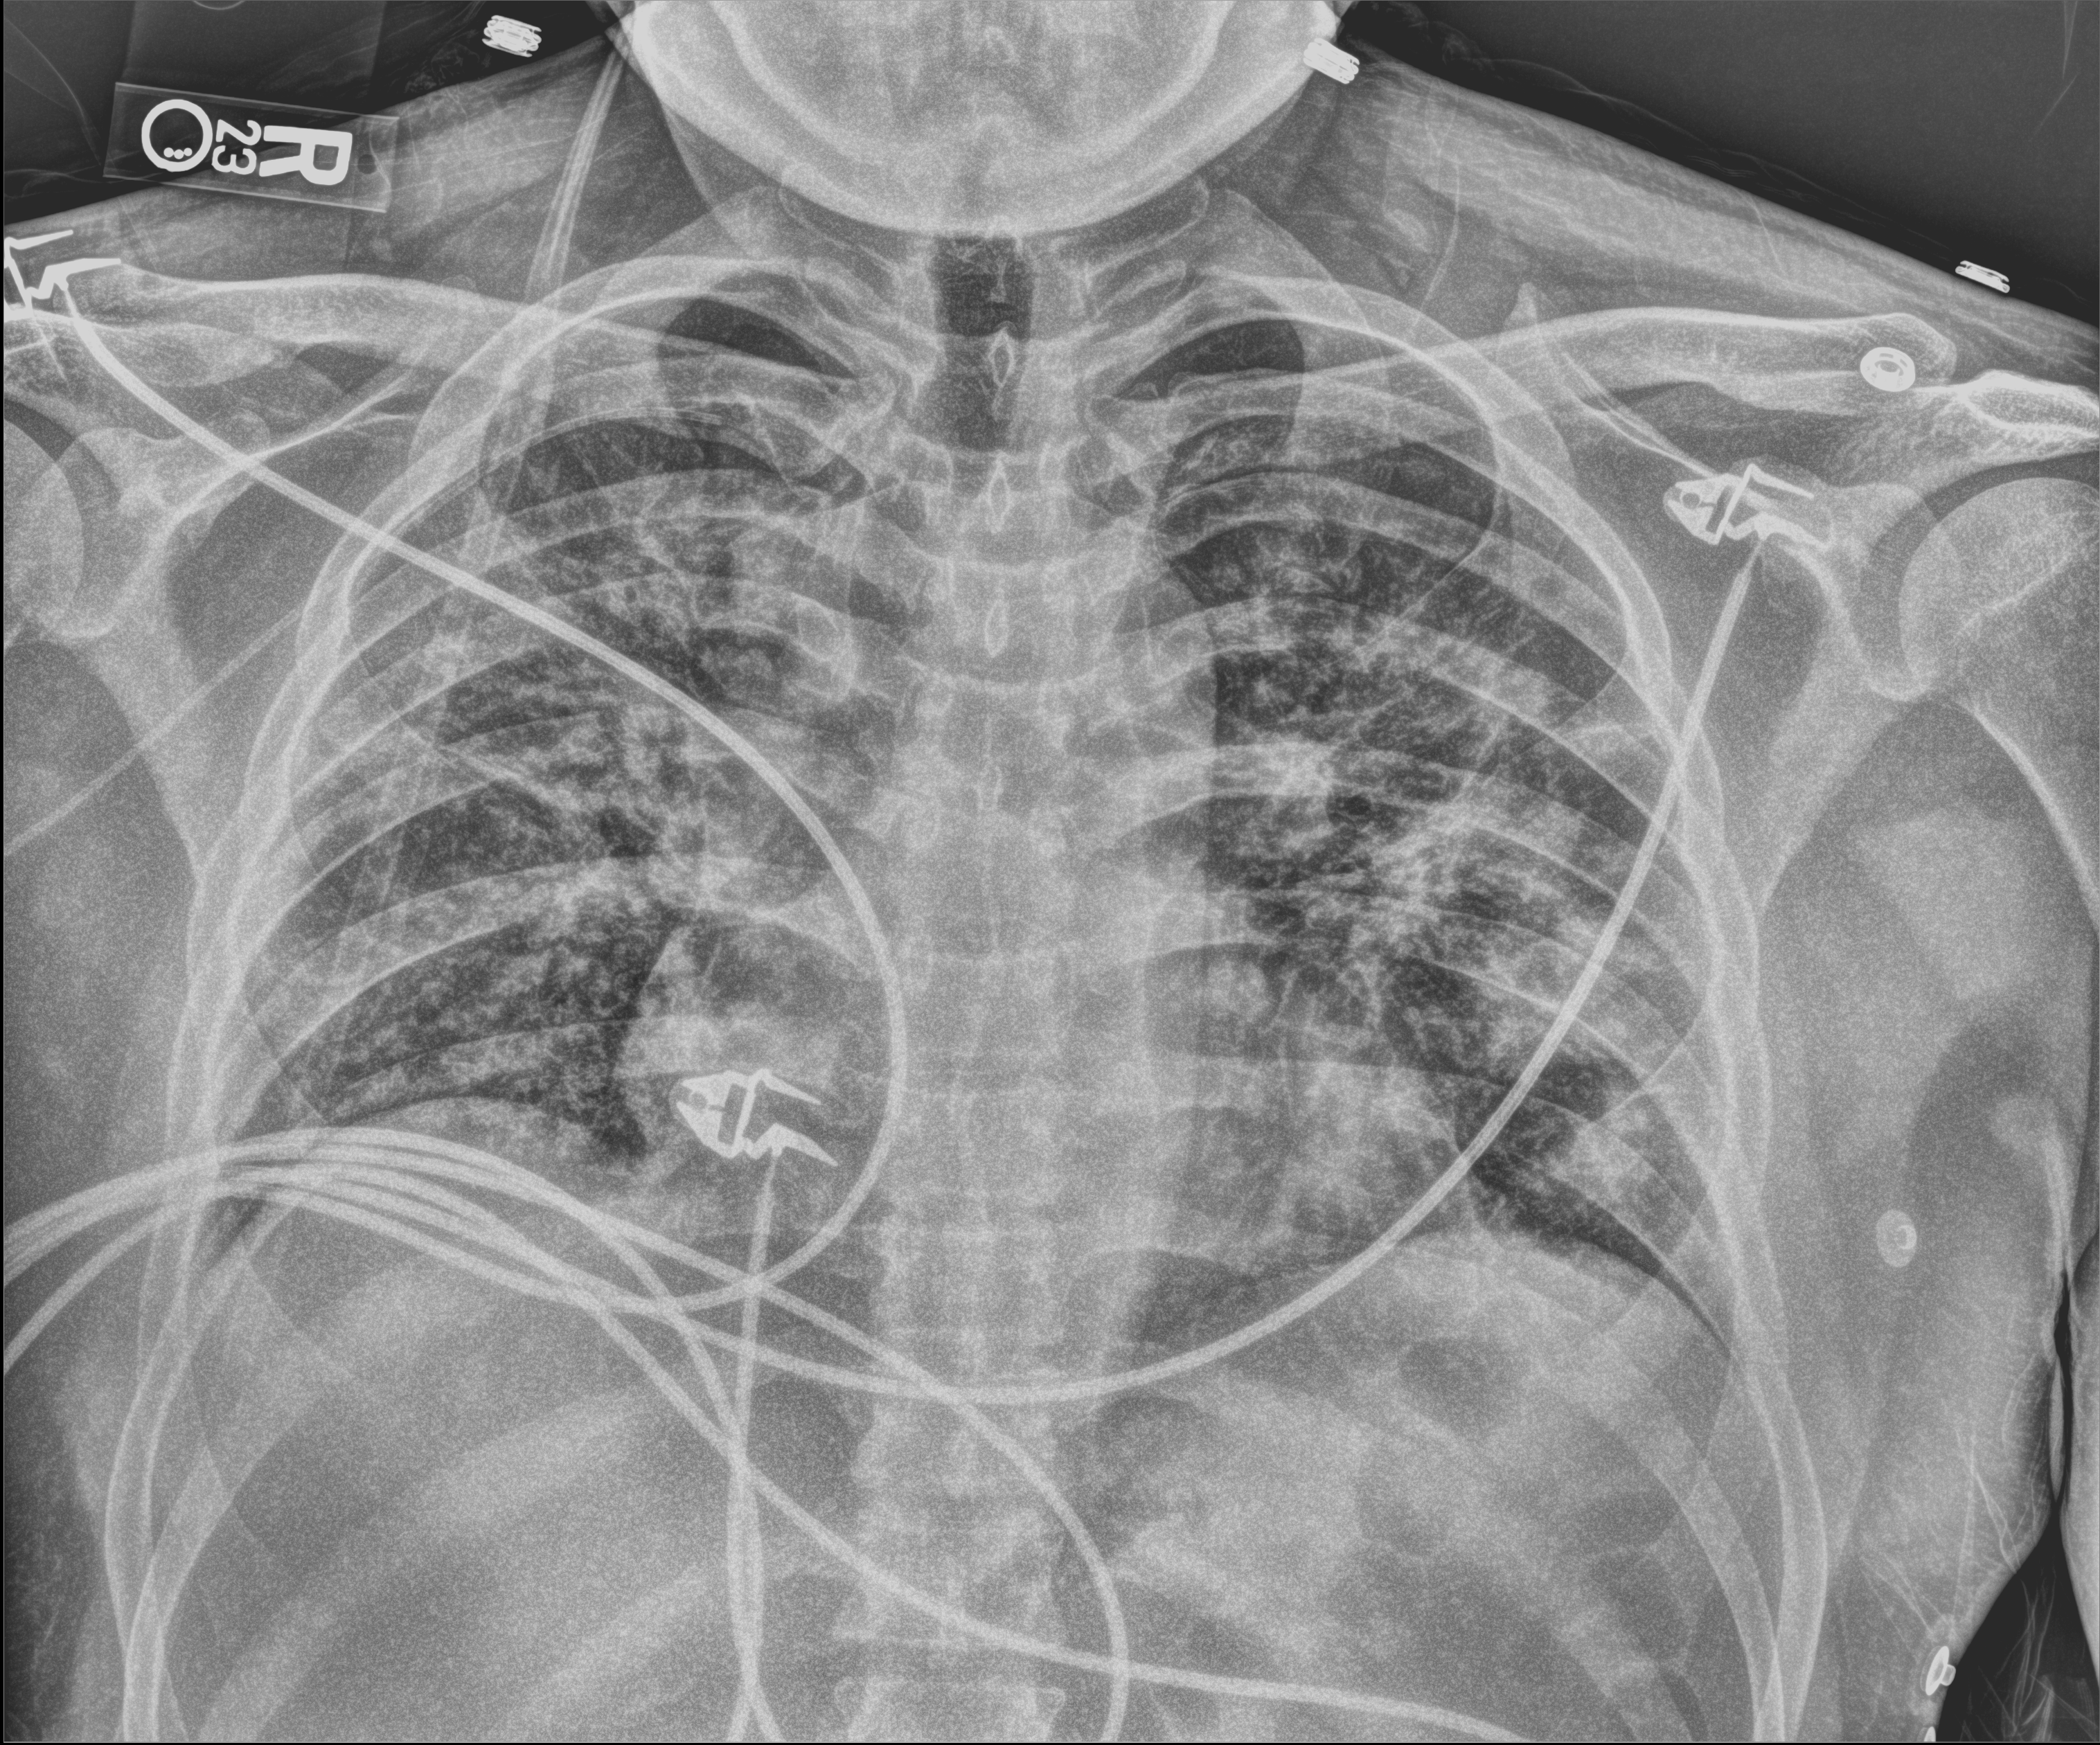
Chest X-ray (portable). Patient hospitalised with COVID-19; male, aged 18–59 years.
From the hospital-stay record, not from the radiograph (when in the stay this image was taken is not recorded):
- mechanically ventilated during this hospital stay: no
- length of hospital stay: 10 days
- admitted to intensive care during this hospital stay: no